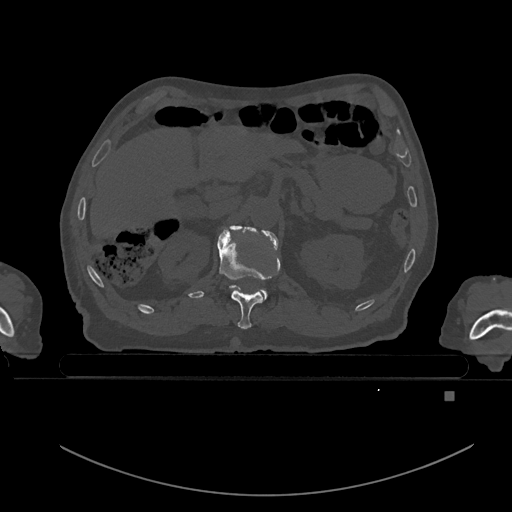
CT including the spine, one axial slice; position 4 of 969 along the scan axis; bone window (W 1800 / L 400 HU); 0.5 mm slice thickness; 512 × 512 image matrix. Patient: male, 82 years. From the clinical record (not read from this slice): primary cancer: prostate.
Outlined on this slice (semi-automatically segmented with operator editing):
- T11 vertebra: box from (x=217, y=227) to (x=279, y=329) px